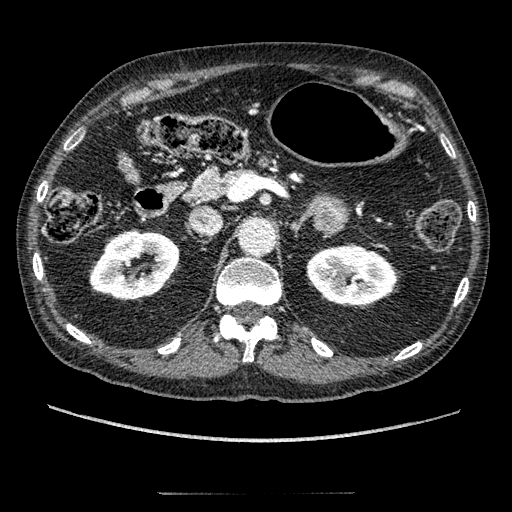
Contrast-enhanced abdominal CT, one axial slice; position 124 of 274 along the scan axis; reconstruction kernel STANDARD; 120 kVp; intravenous contrast given; soft-tissue window (W 400 / L 40 HU); 1.25 mm slice thickness; 512 × 512 image matrix, field of view 381 × 381 mm. Patient: male, 69 years. Case-level facts recorded for this patient, not image findings: diagnosis: adrenocortical carcinoma; tumour side: left adrenal; tumour size at pathology: 6.1 cm; Ki-67 index: 10 %; stage (as recorded): 3.
Structures marked on this image (semi-automatic segmentation, software-assisted and operator-edited):
- mass: bounding box (x1, y1, x2, y2) in pixels: (315, 196, 347, 232)